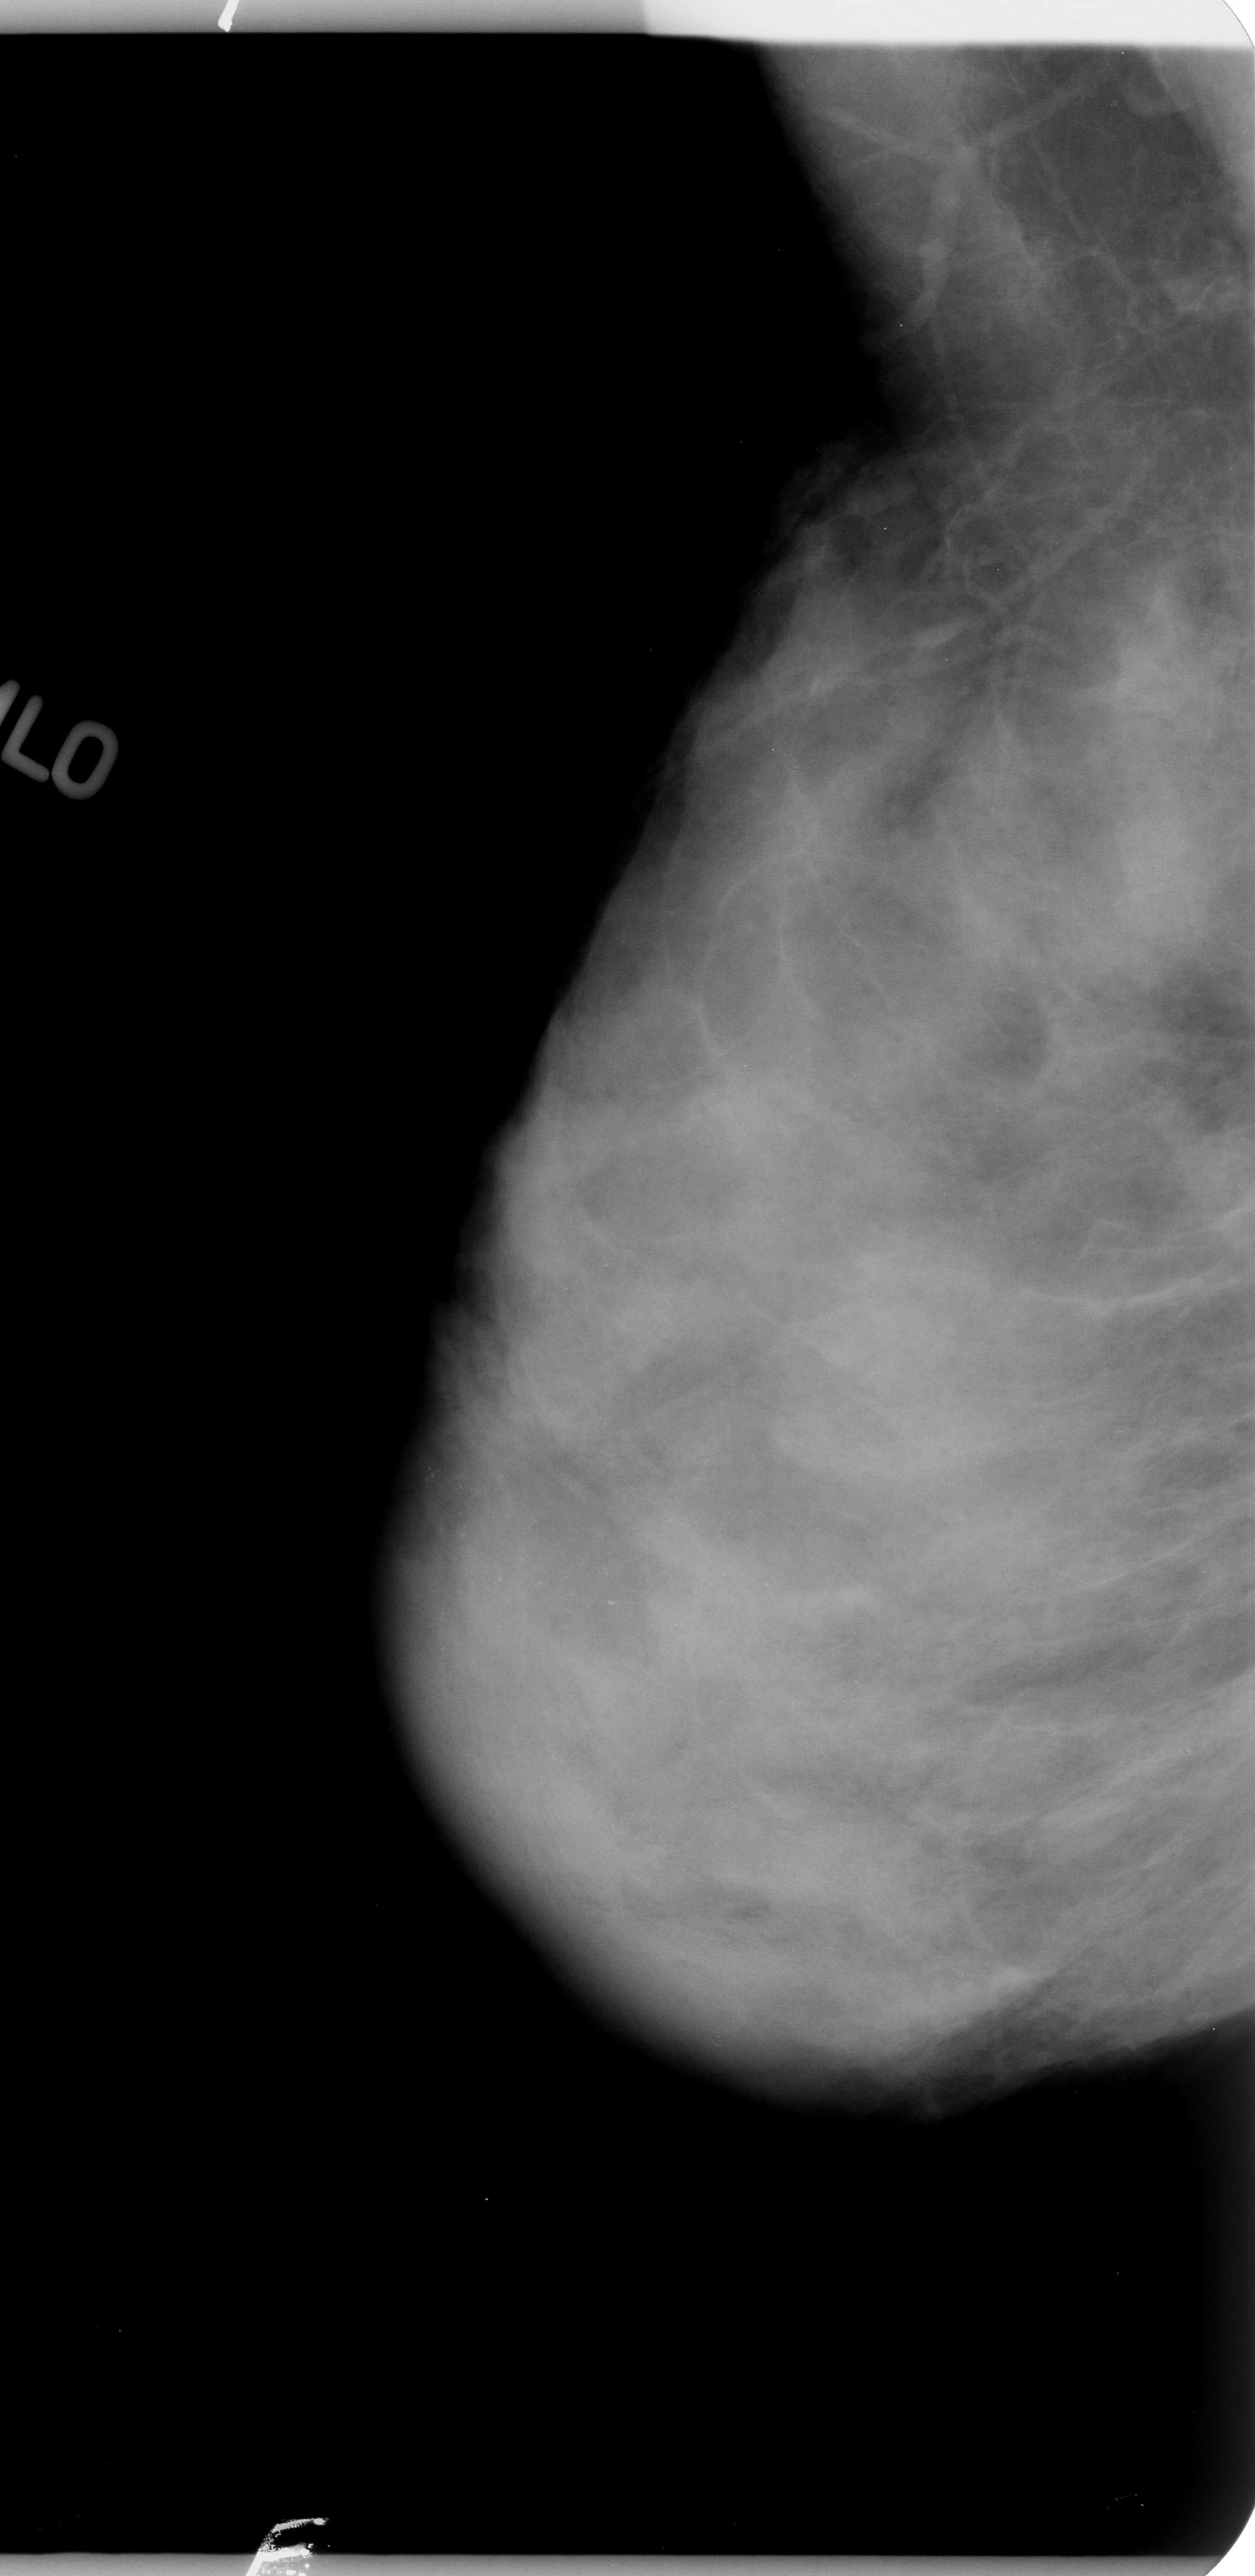
Scanned film-screen mammogram; right breast; MLO view; BI-RADS breast density category 4 (scale 1–4).
Calcifications, morphology pleomorphic, distribution regional; BI-RADS assessment category 4; pathology result (as recorded, not read from the image): benign.